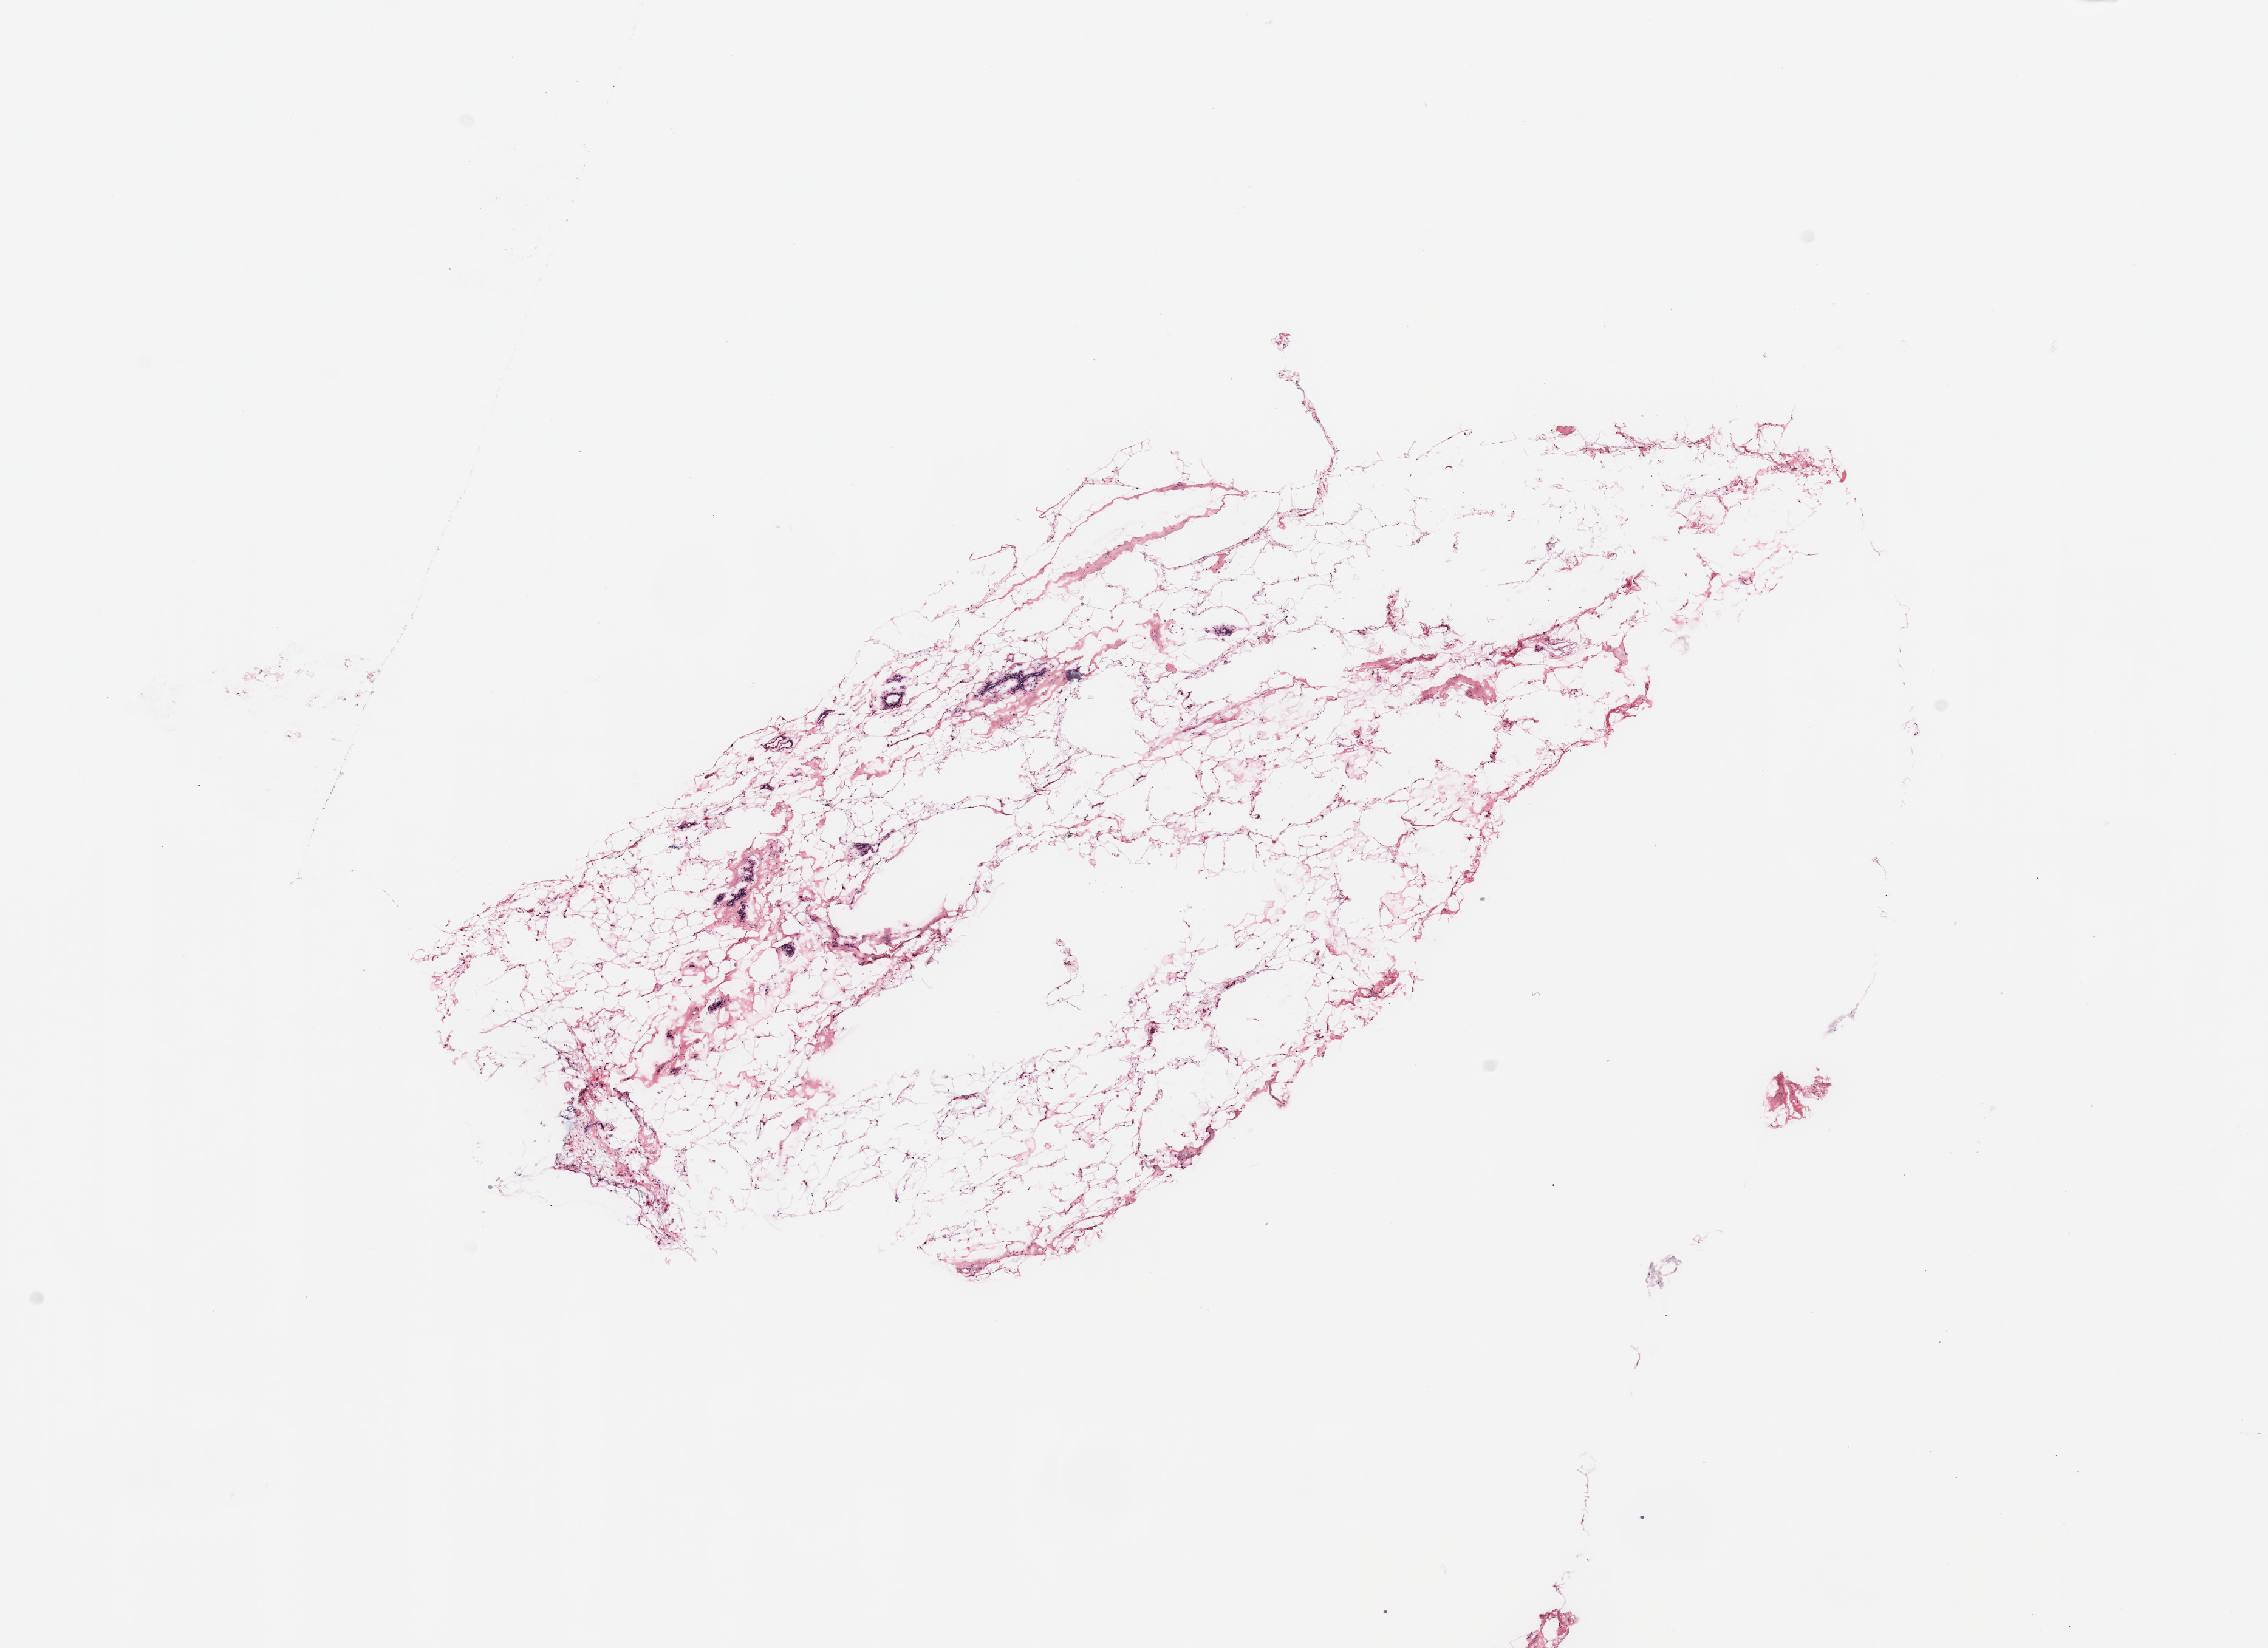
Digitized H&E-stained tissue section (whole slide) — shown as a low-resolution overview of the whole scanned area (about 14.8 x 10.7 mm); tumour tissue sample, breast. Female, 60 y/o.
Histologic diagnosis: Infiltrating duct carcinoma, NOS. AJCC pathologic stage: IIA.